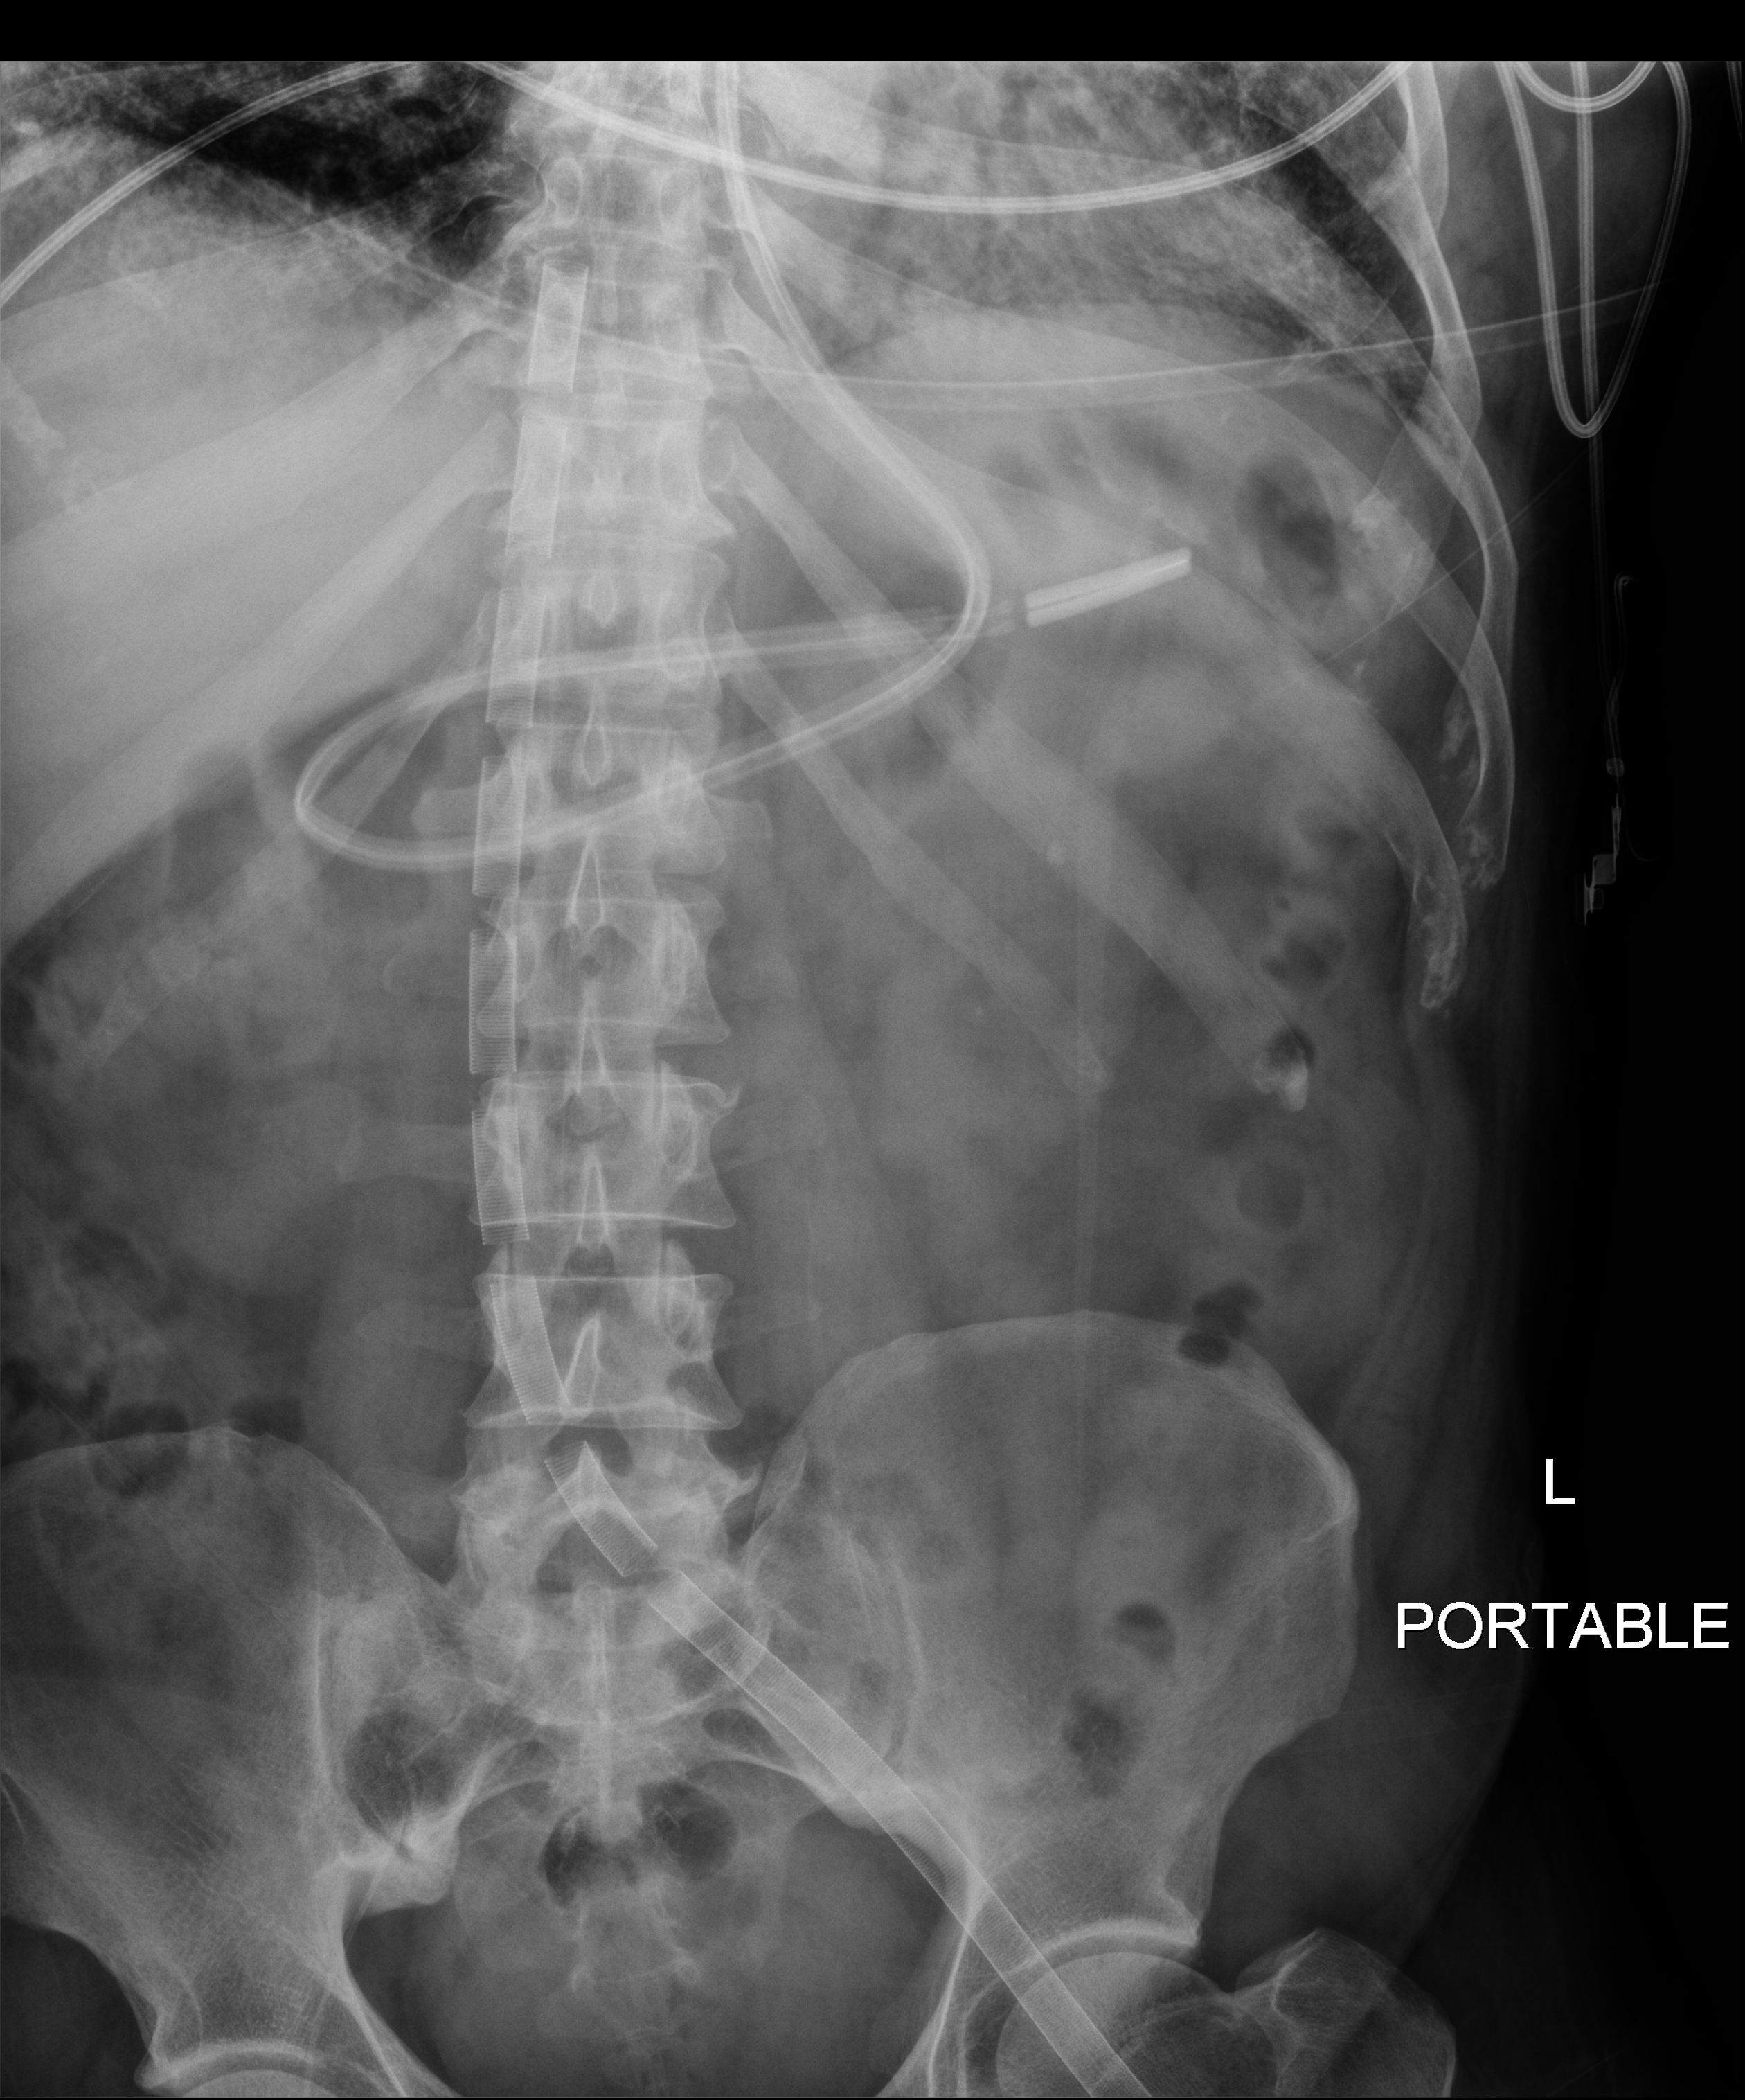
Portable abdomen radiograph; anteroposterior (AP) projection. Patient hospitalised with COVID-19; male, aged 18–59 years.
From the hospital-stay record, not from the radiograph (when in the stay this image was taken is not recorded):
- mechanically ventilated during this hospital stay: yes
- admitted to intensive care during this hospital stay: yes